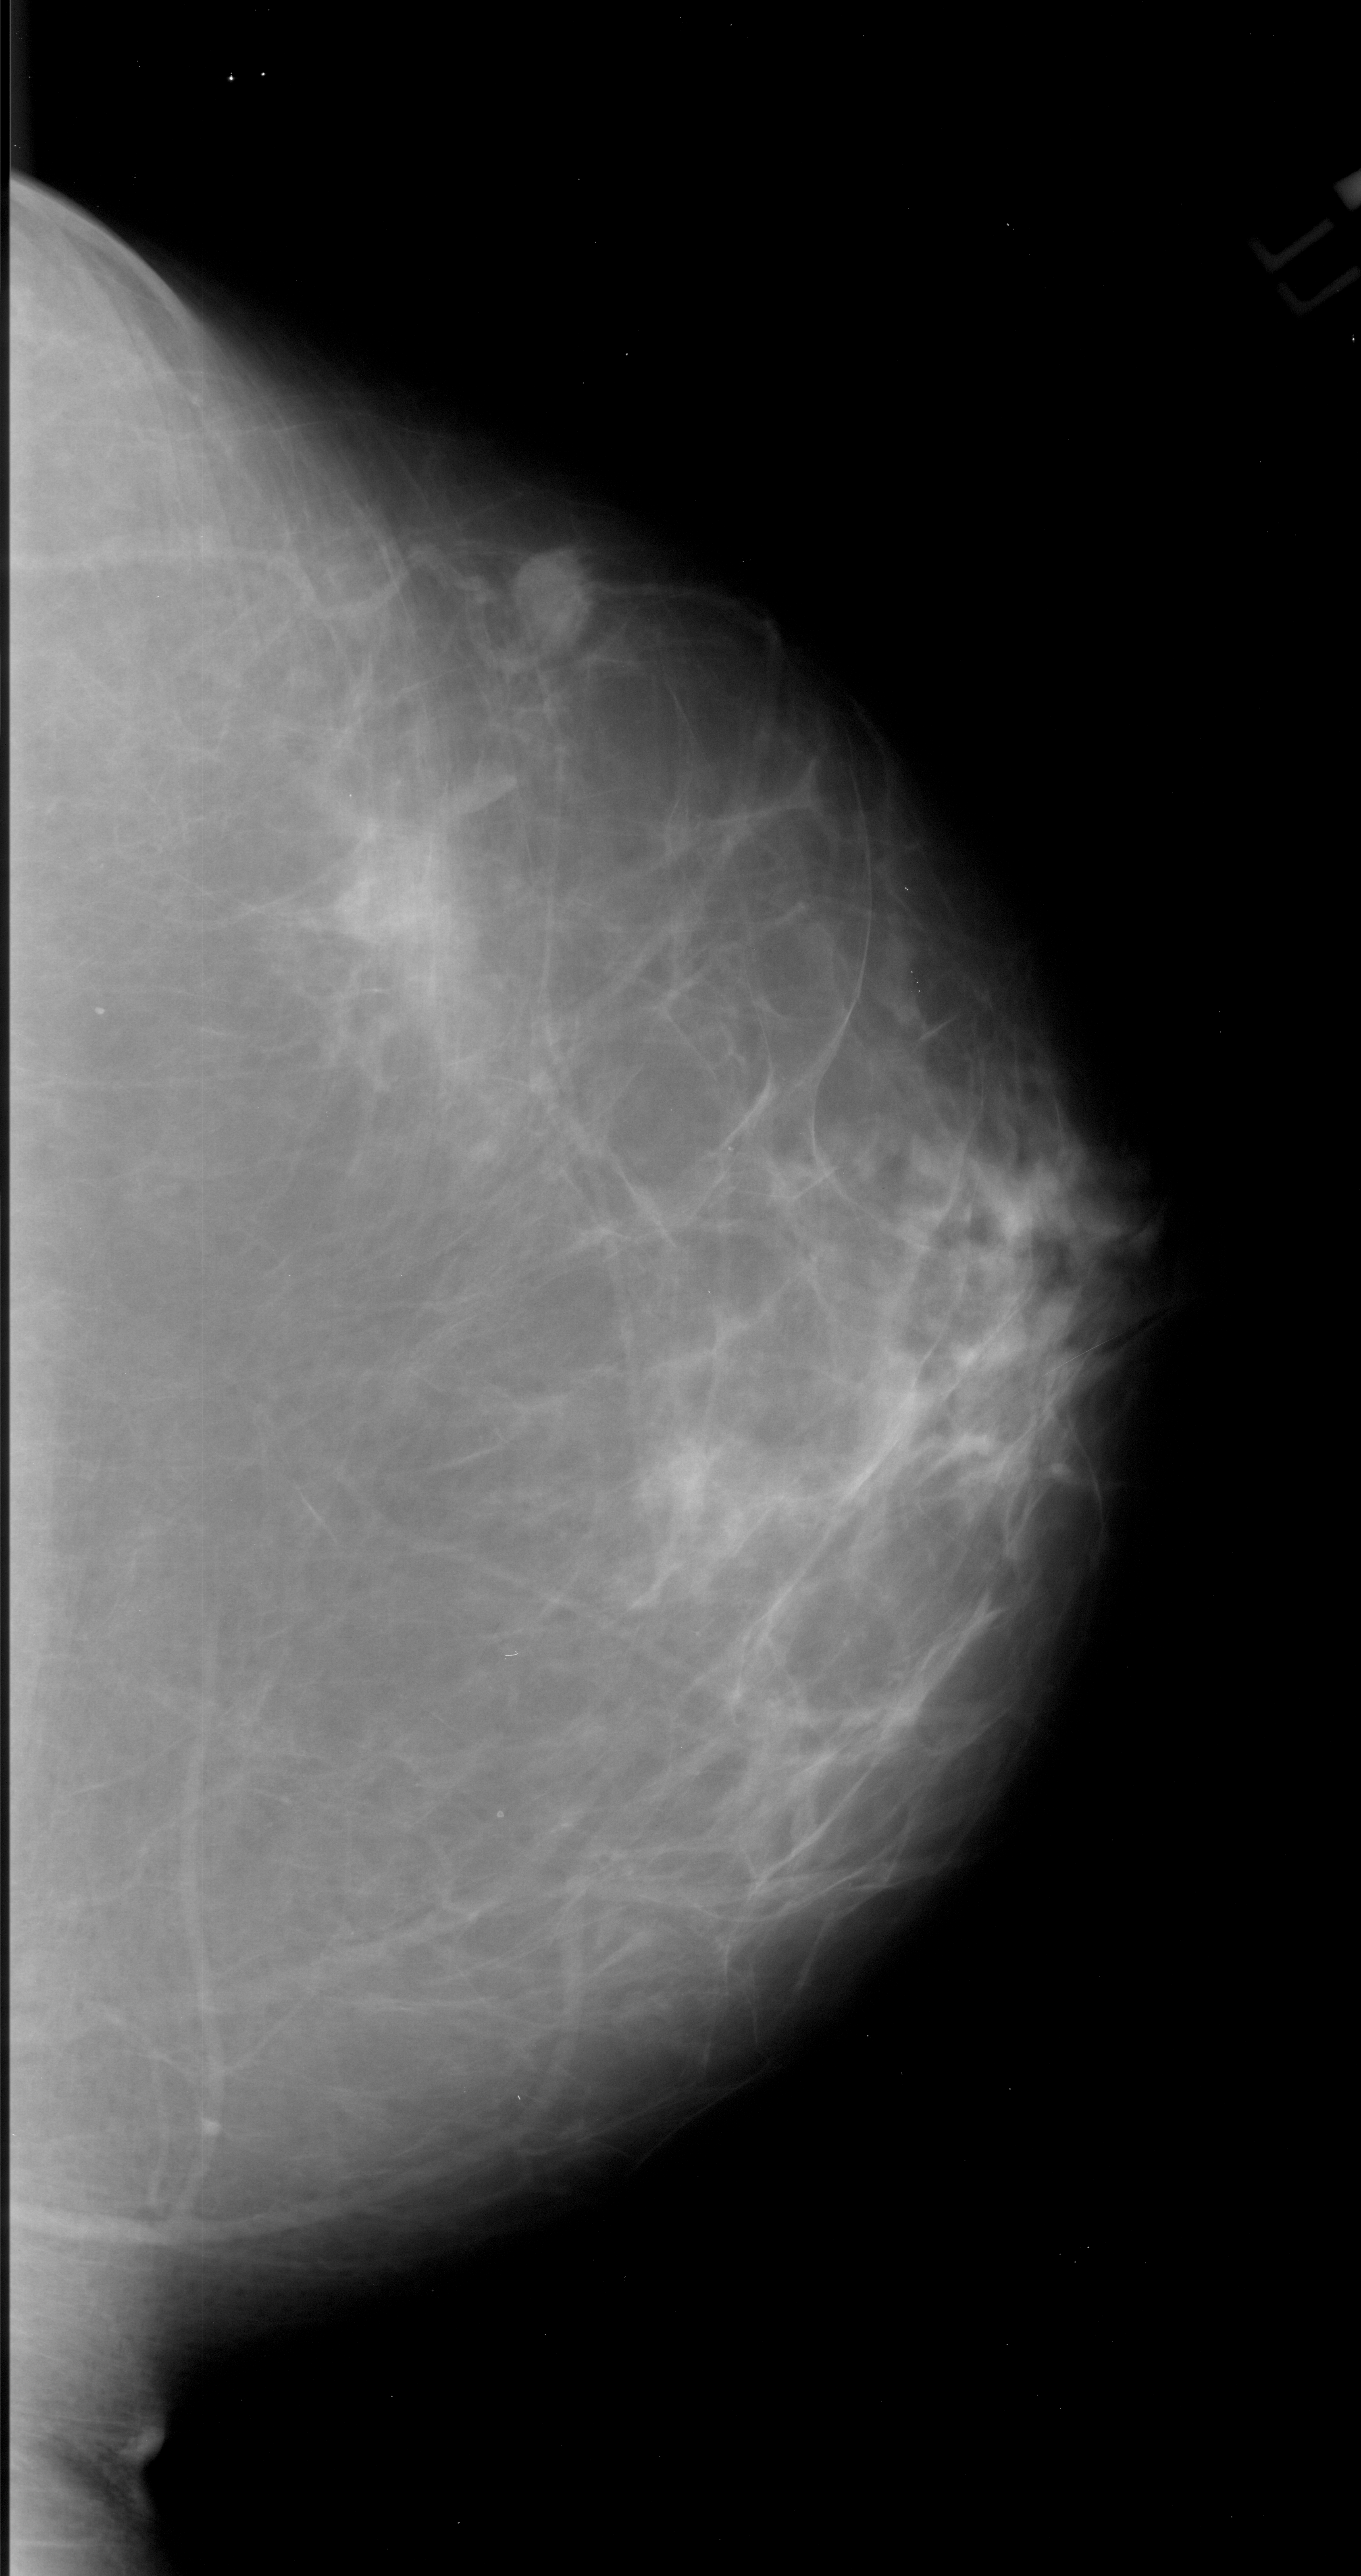
Mammogram (digitized film), right breast, CC view.
Finding: mass, shape round, margins ill defined; BI-RADS assessment category 4; subtlety rating 4 on a 1 (subtle) to 5 (obvious) scale; pathology (as recorded): malignant.